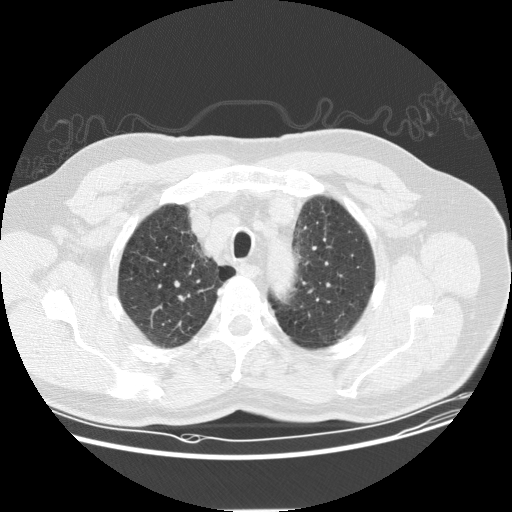
Axial slice from a low-dose chest CT screening exam. First (baseline) screen. Lung window (W 1500 / L -600 HU). 2.5 mm slice thickness. Standard (soft-tissue) reconstruction kernel (STANDARD). Male, age 61 years at enrolment.
Lesion marked by an expert reader, bounding box [x1, y1, x2, y2] px = [159, 285, 196, 321]. No non-calcified nodule or mass ≥4 mm was recorded by the screening reader at this exam. Official screen result: negative screen, minor abnormalities not suspicious for lung cancer. Participant outcome: lung cancer diagnosed 832 days after this screen — squamous cell carcinoma, NOS, right upper lobe, moderately differentiated (G2), stage IA (AJCC 6th edition), 10 mm at pathology.